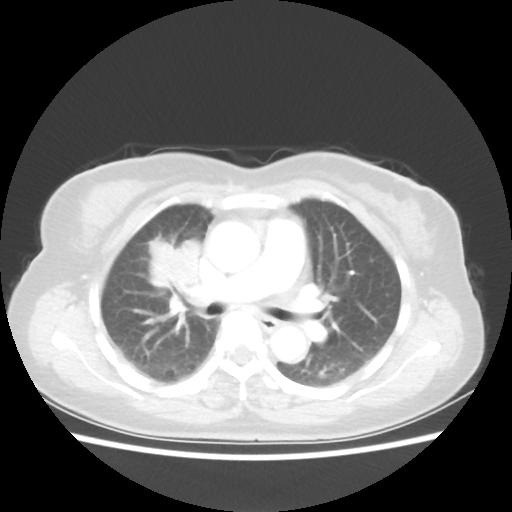
Chest CT, one axial slice. Position 33 of 55 along the scan axis. 80 kVp. Lung window (W 1500 / L -600 HU). 512 × 512 image matrix. Female patient, age 62 years. From the clinical record (not read from this slice): clinical TNM (as recorded): T4 N3 M0.
Outlined on this slice (rectangle marked by the reading radiologist):
- lung tumour (recorded histology: squamous cell carcinoma): box from (x=136, y=224) to (x=222, y=309) px